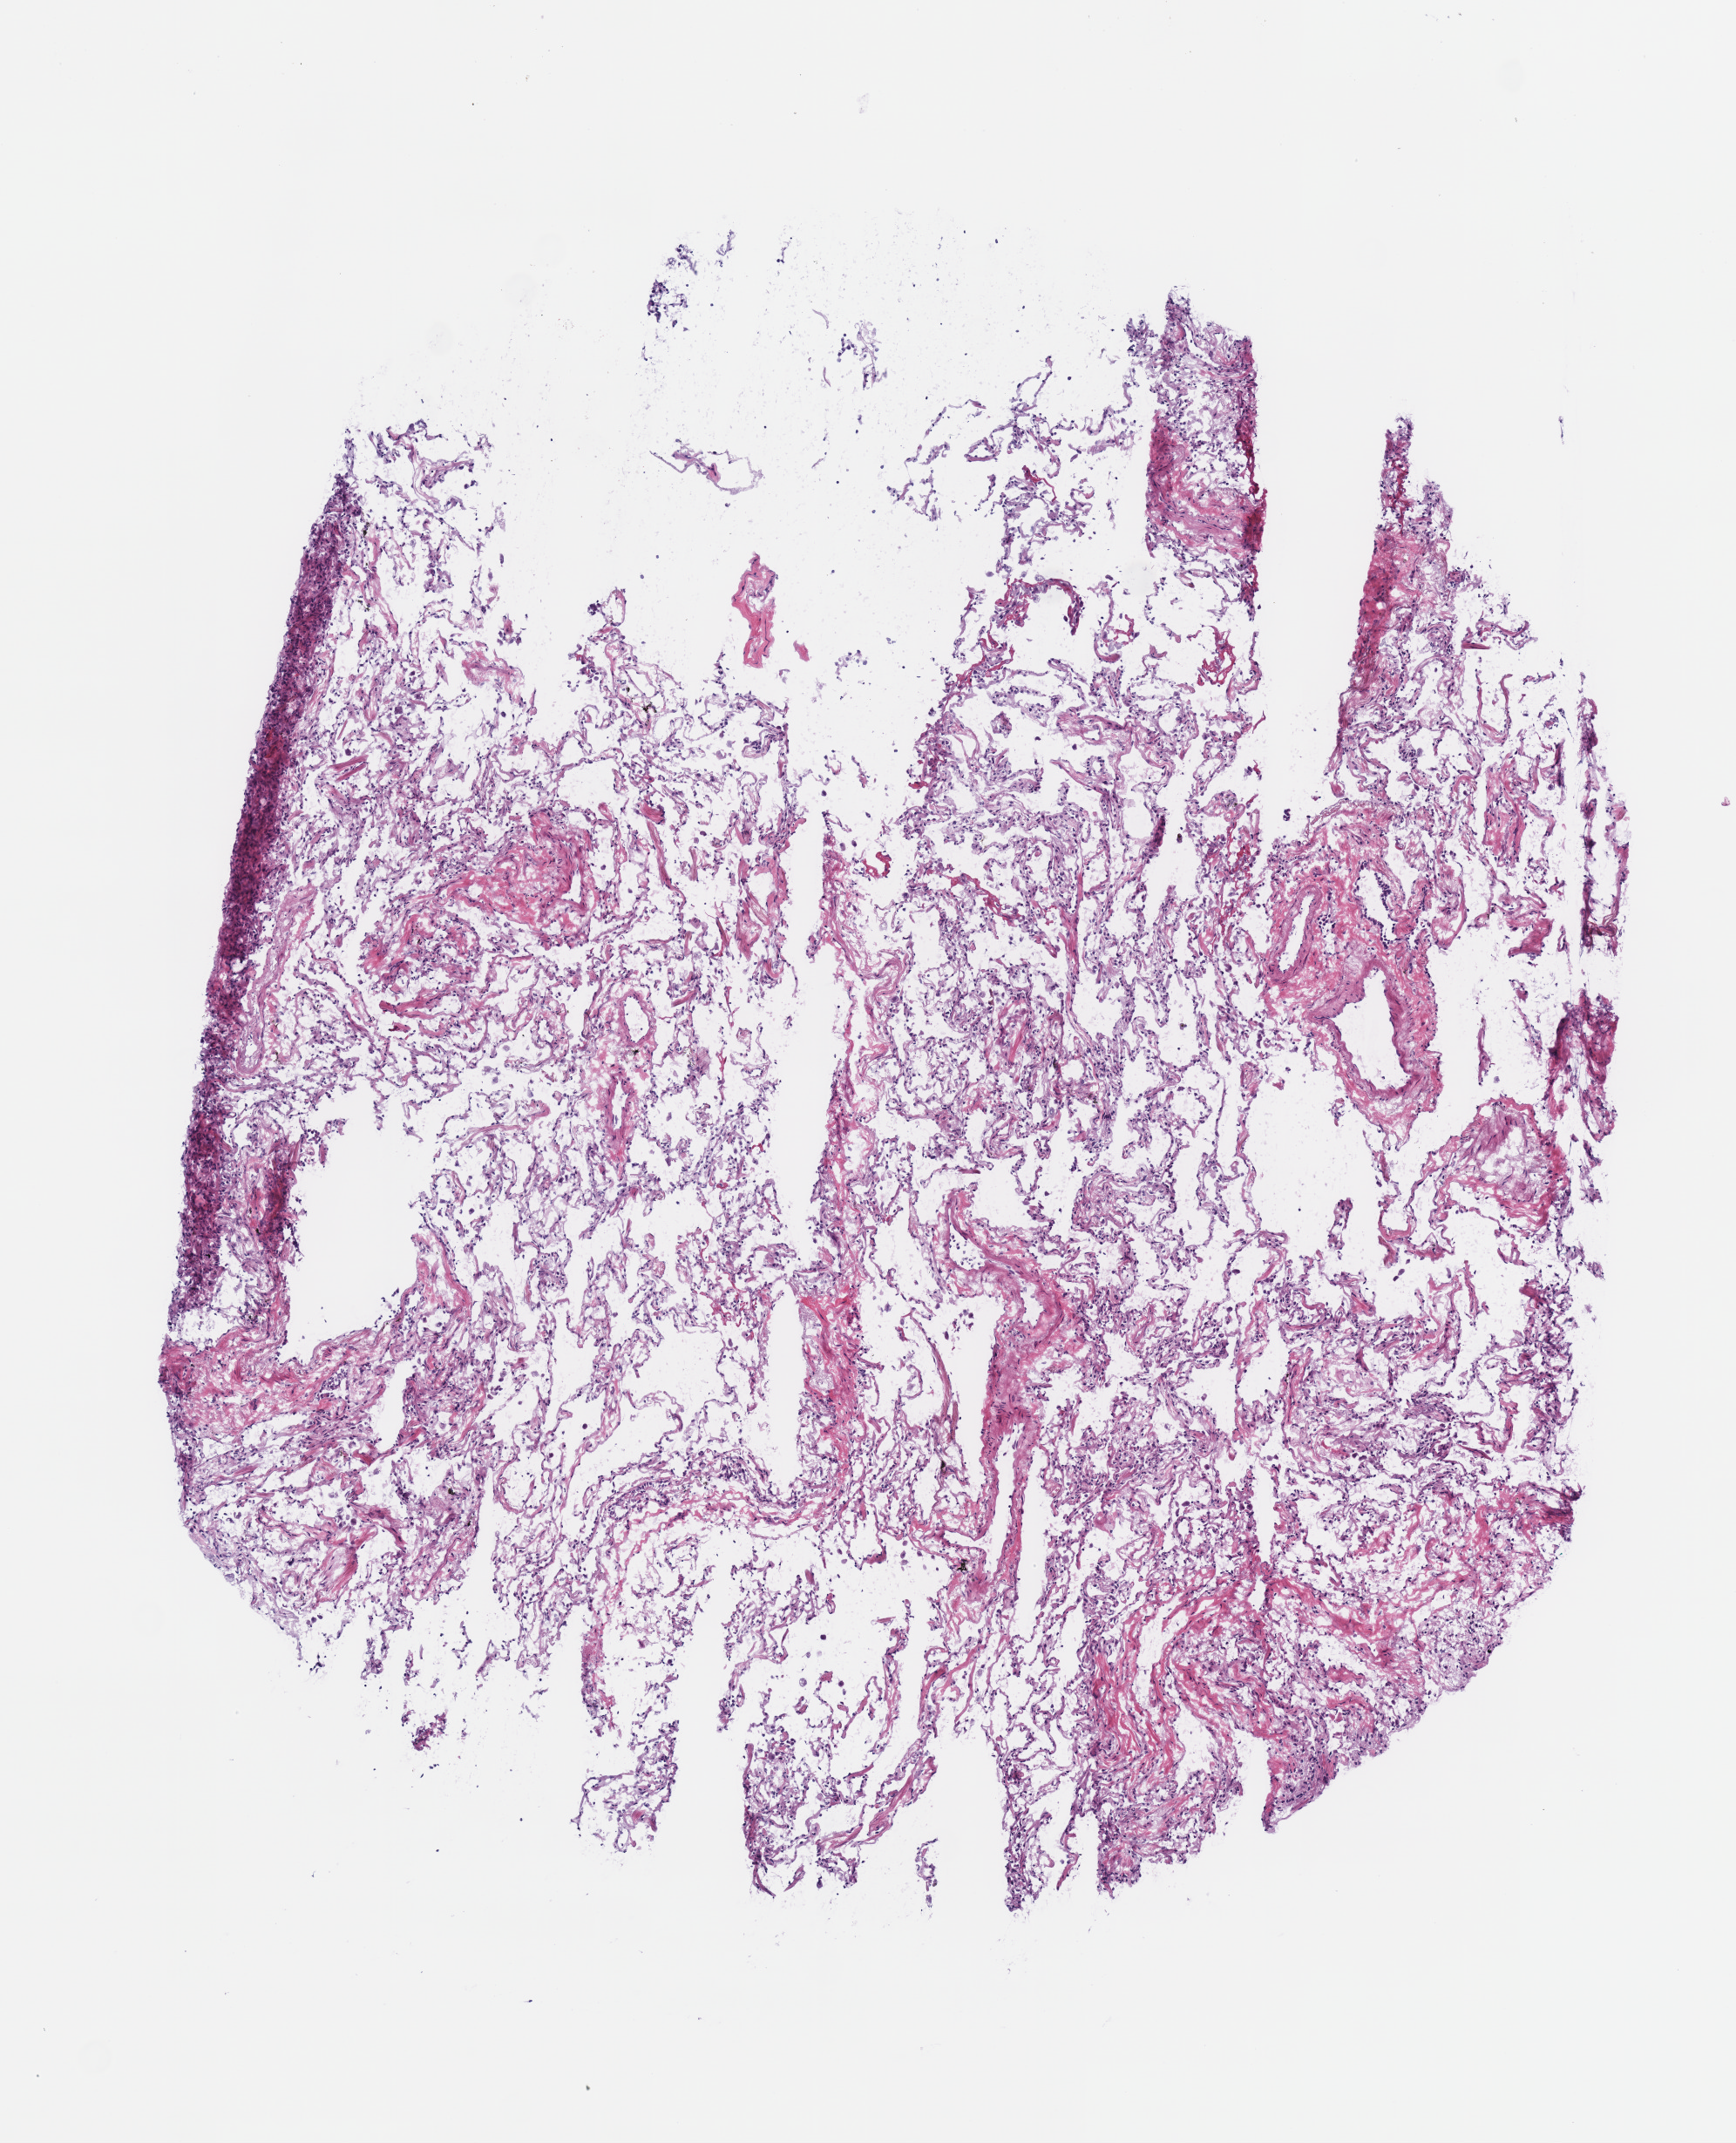
H&E whole-slide image, a low-resolution overview of the entire scanned area, about 3.9 x 4.8 mm. Frozen section. Solid tissue normal (non-tumour tissue) sample from the lung. Patient: male, age at initial diagnosis 78 years.
This section: solid tissue normal (non-tumour) sample from the same patient. Patient diagnosis: Squamous cell carcinoma, NOS.